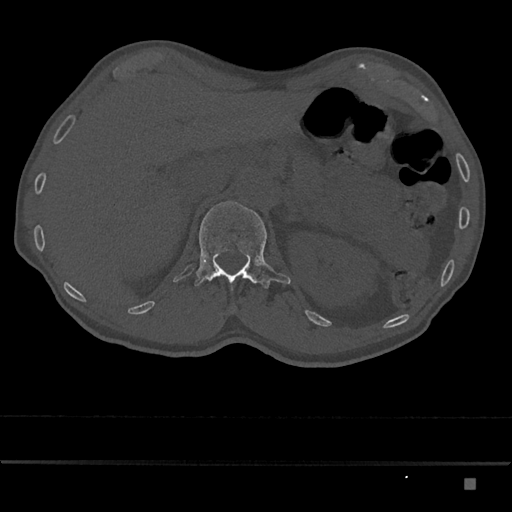
CT including the spine, one axial slice; position 552 of 797 along the scan axis; reconstruction kernel Br40s/3; 120 kVp; bone window (W 1800 / L 400 HU); 512 × 512 image matrix, field of view 390 × 390 mm. Patient: male, 72 years. Case-level facts recorded for this patient, not image findings: primary cancer: prostate.
Outlined on this slice (semi-automatic segmentation, software-assisted and operator-edited):
- L1 vertebra: bounding box <194,201,291,290> (left, top, right, bottom; pixels)